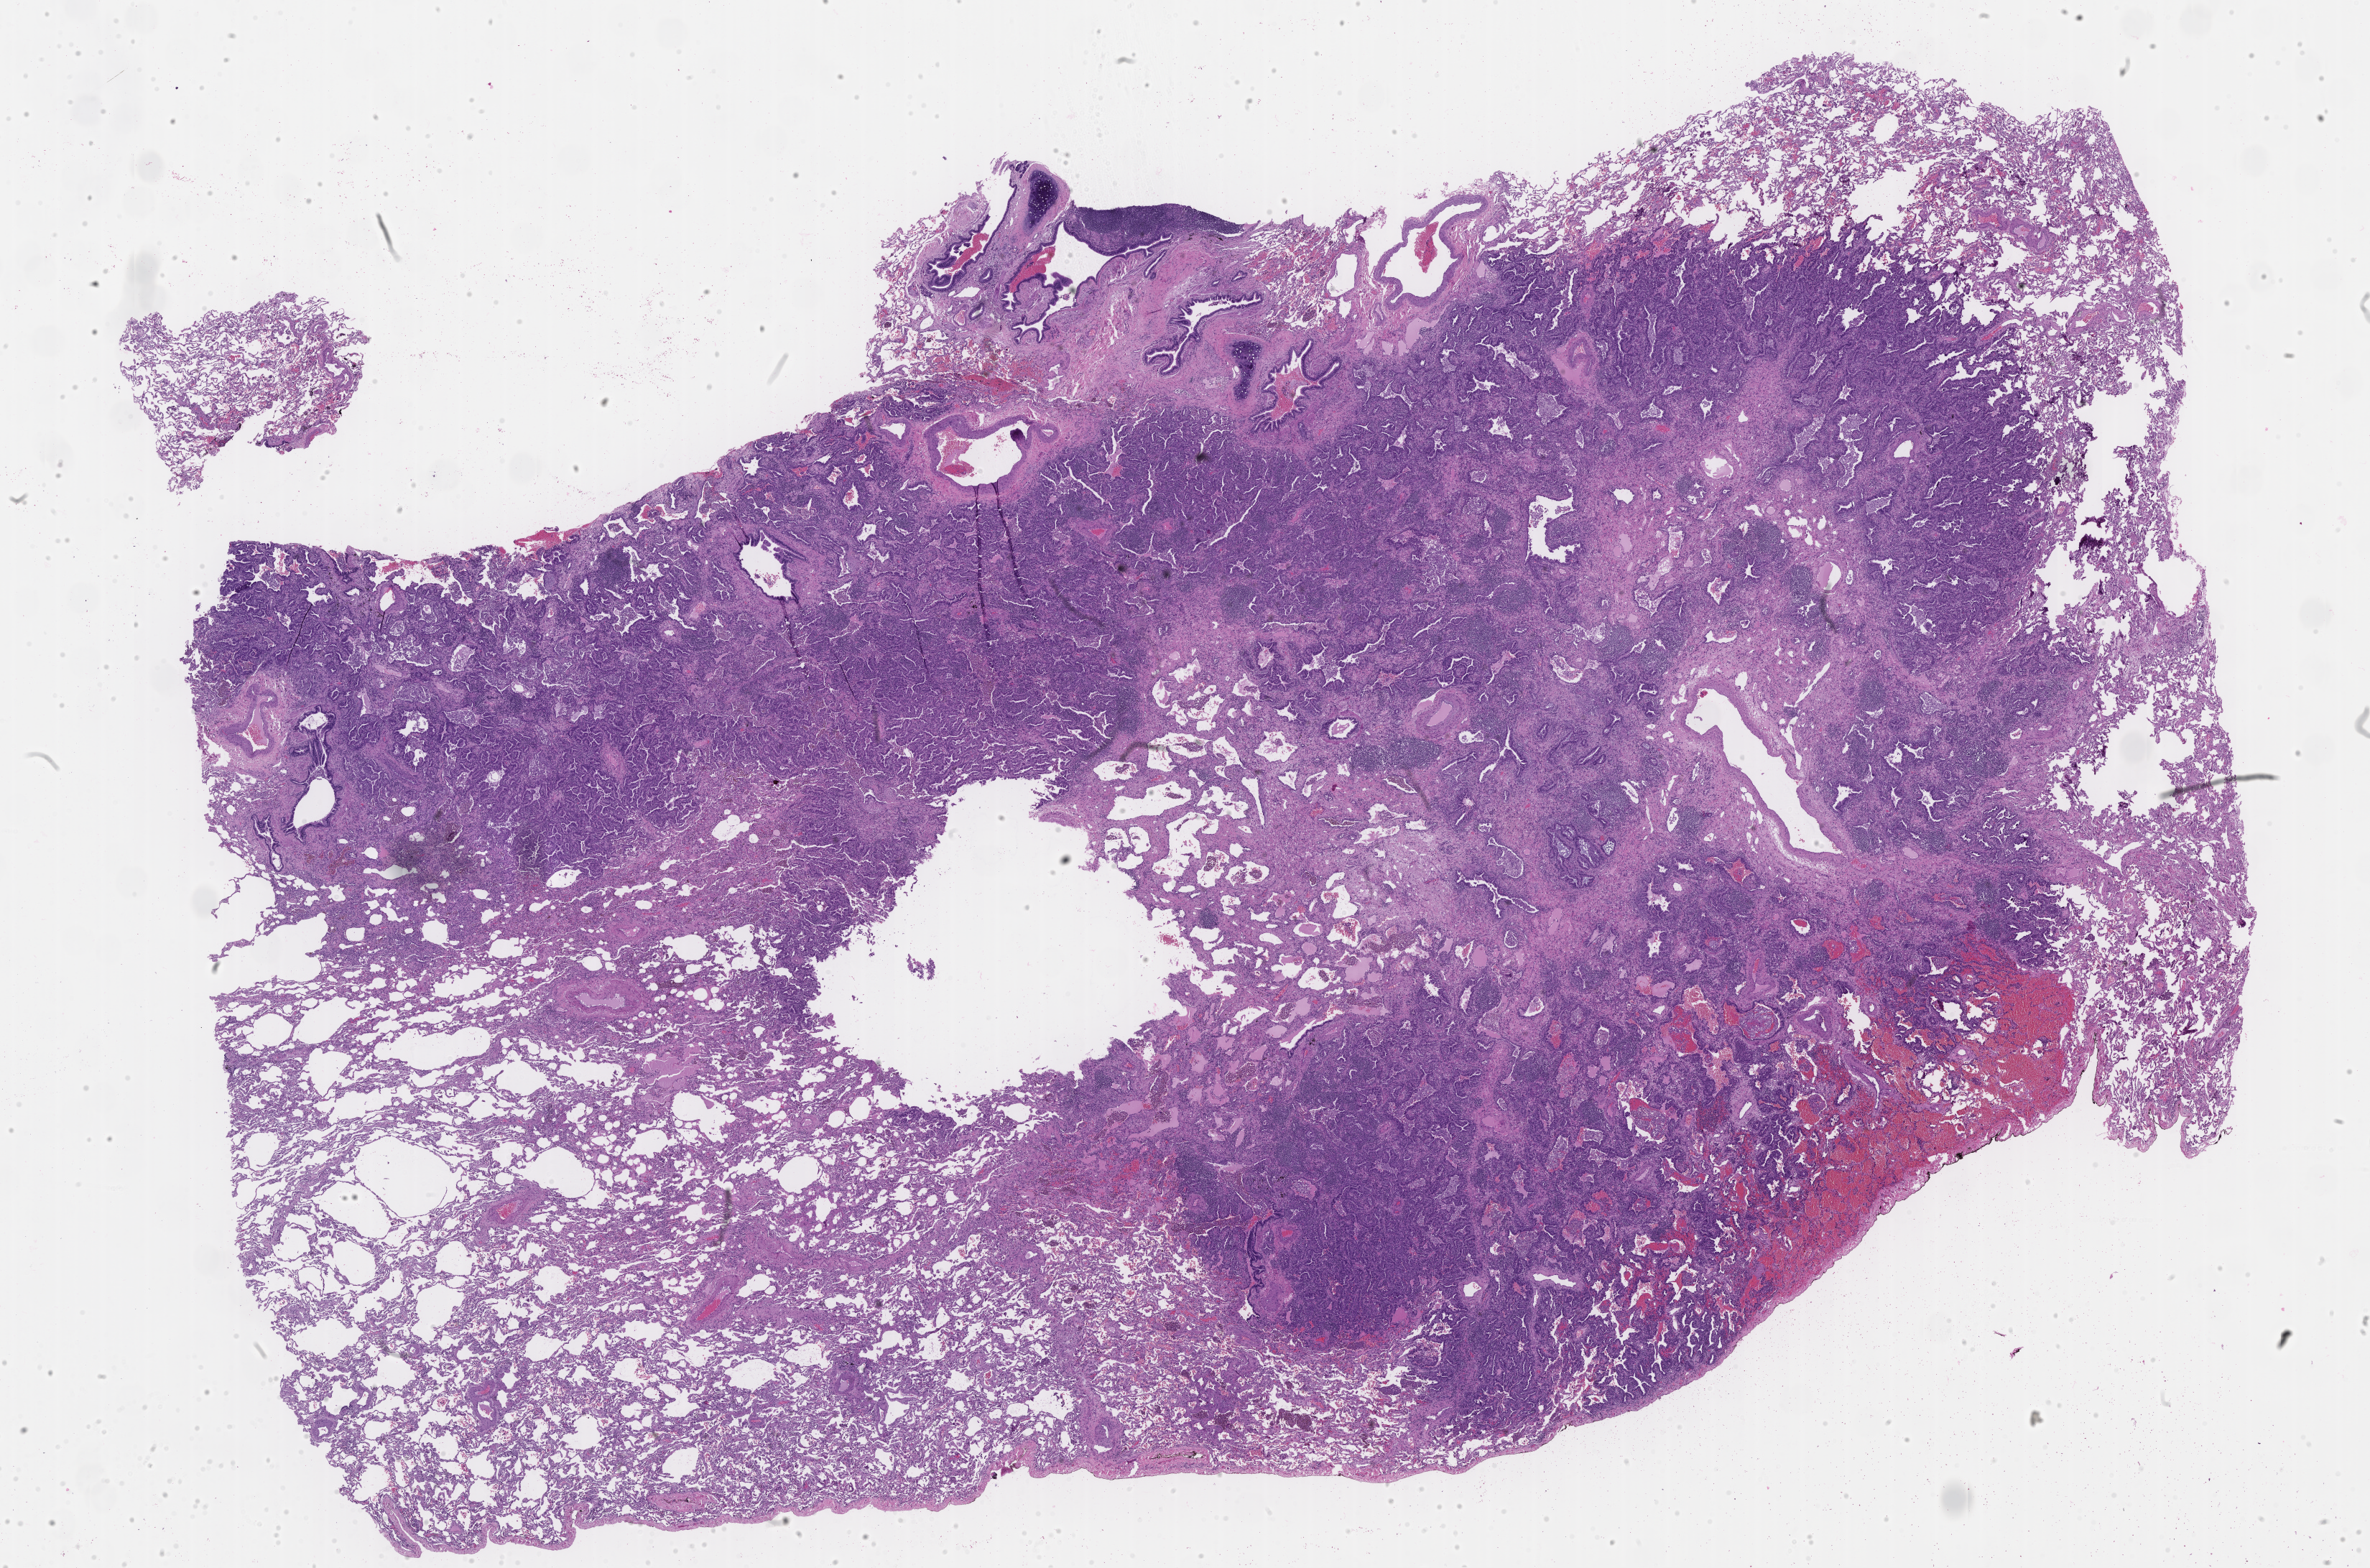
Digitized H&E tissue section (whole slide), low-resolution overview of the scanned area, about 26.6 x 17.6 mm (slide scanned at 40x); tumour tissue sample, sampled site: lung. Patient: female, age 54 years. Histologic grade: G1 (well differentiated). Slide review estimates, as recorded: tumour nuclei 60%, necrosis 0%.
• AJCC pathologic stage: IA3
• histologic diagnosis: Adenocarcinoma, NOS